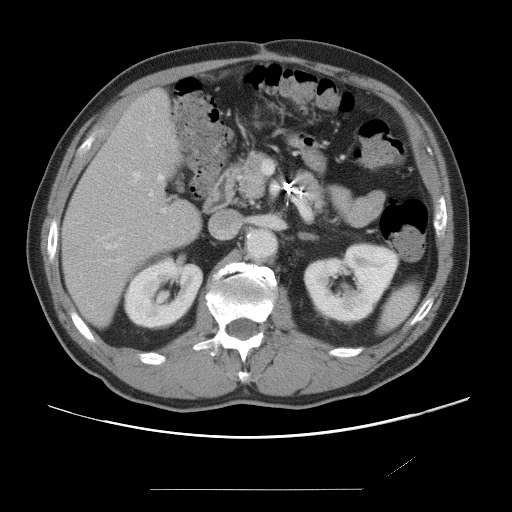
Contrast-enhanced abdominal CT, one axial slice; 120 kVp; intravenous contrast given; soft-tissue window (W 400 / L 40 HU); 5 mm slice thickness; 512 × 512 image matrix, field of view 406 × 406 mm. Male patient, age 74 years. Case-level facts recorded for this patient, not image findings: diagnosis: colorectal cancer liver metastases, imaged before liver resection; multiple liver metastases: yes; largest metastasis: 1.1 cm; chemotherapy before resection: yes.
Annotated regions visible in this slice (expert manual segmentation):
- hepatic veins: bounding box <107,137,163,249> (left, top, right, bottom; pixels)
- liver: <65,92,200,325>
- planned liver remnant (the part of the liver to remain after resection): <65,92,200,325>
- portal vein (with intrahepatic branches): <149,160,274,212>